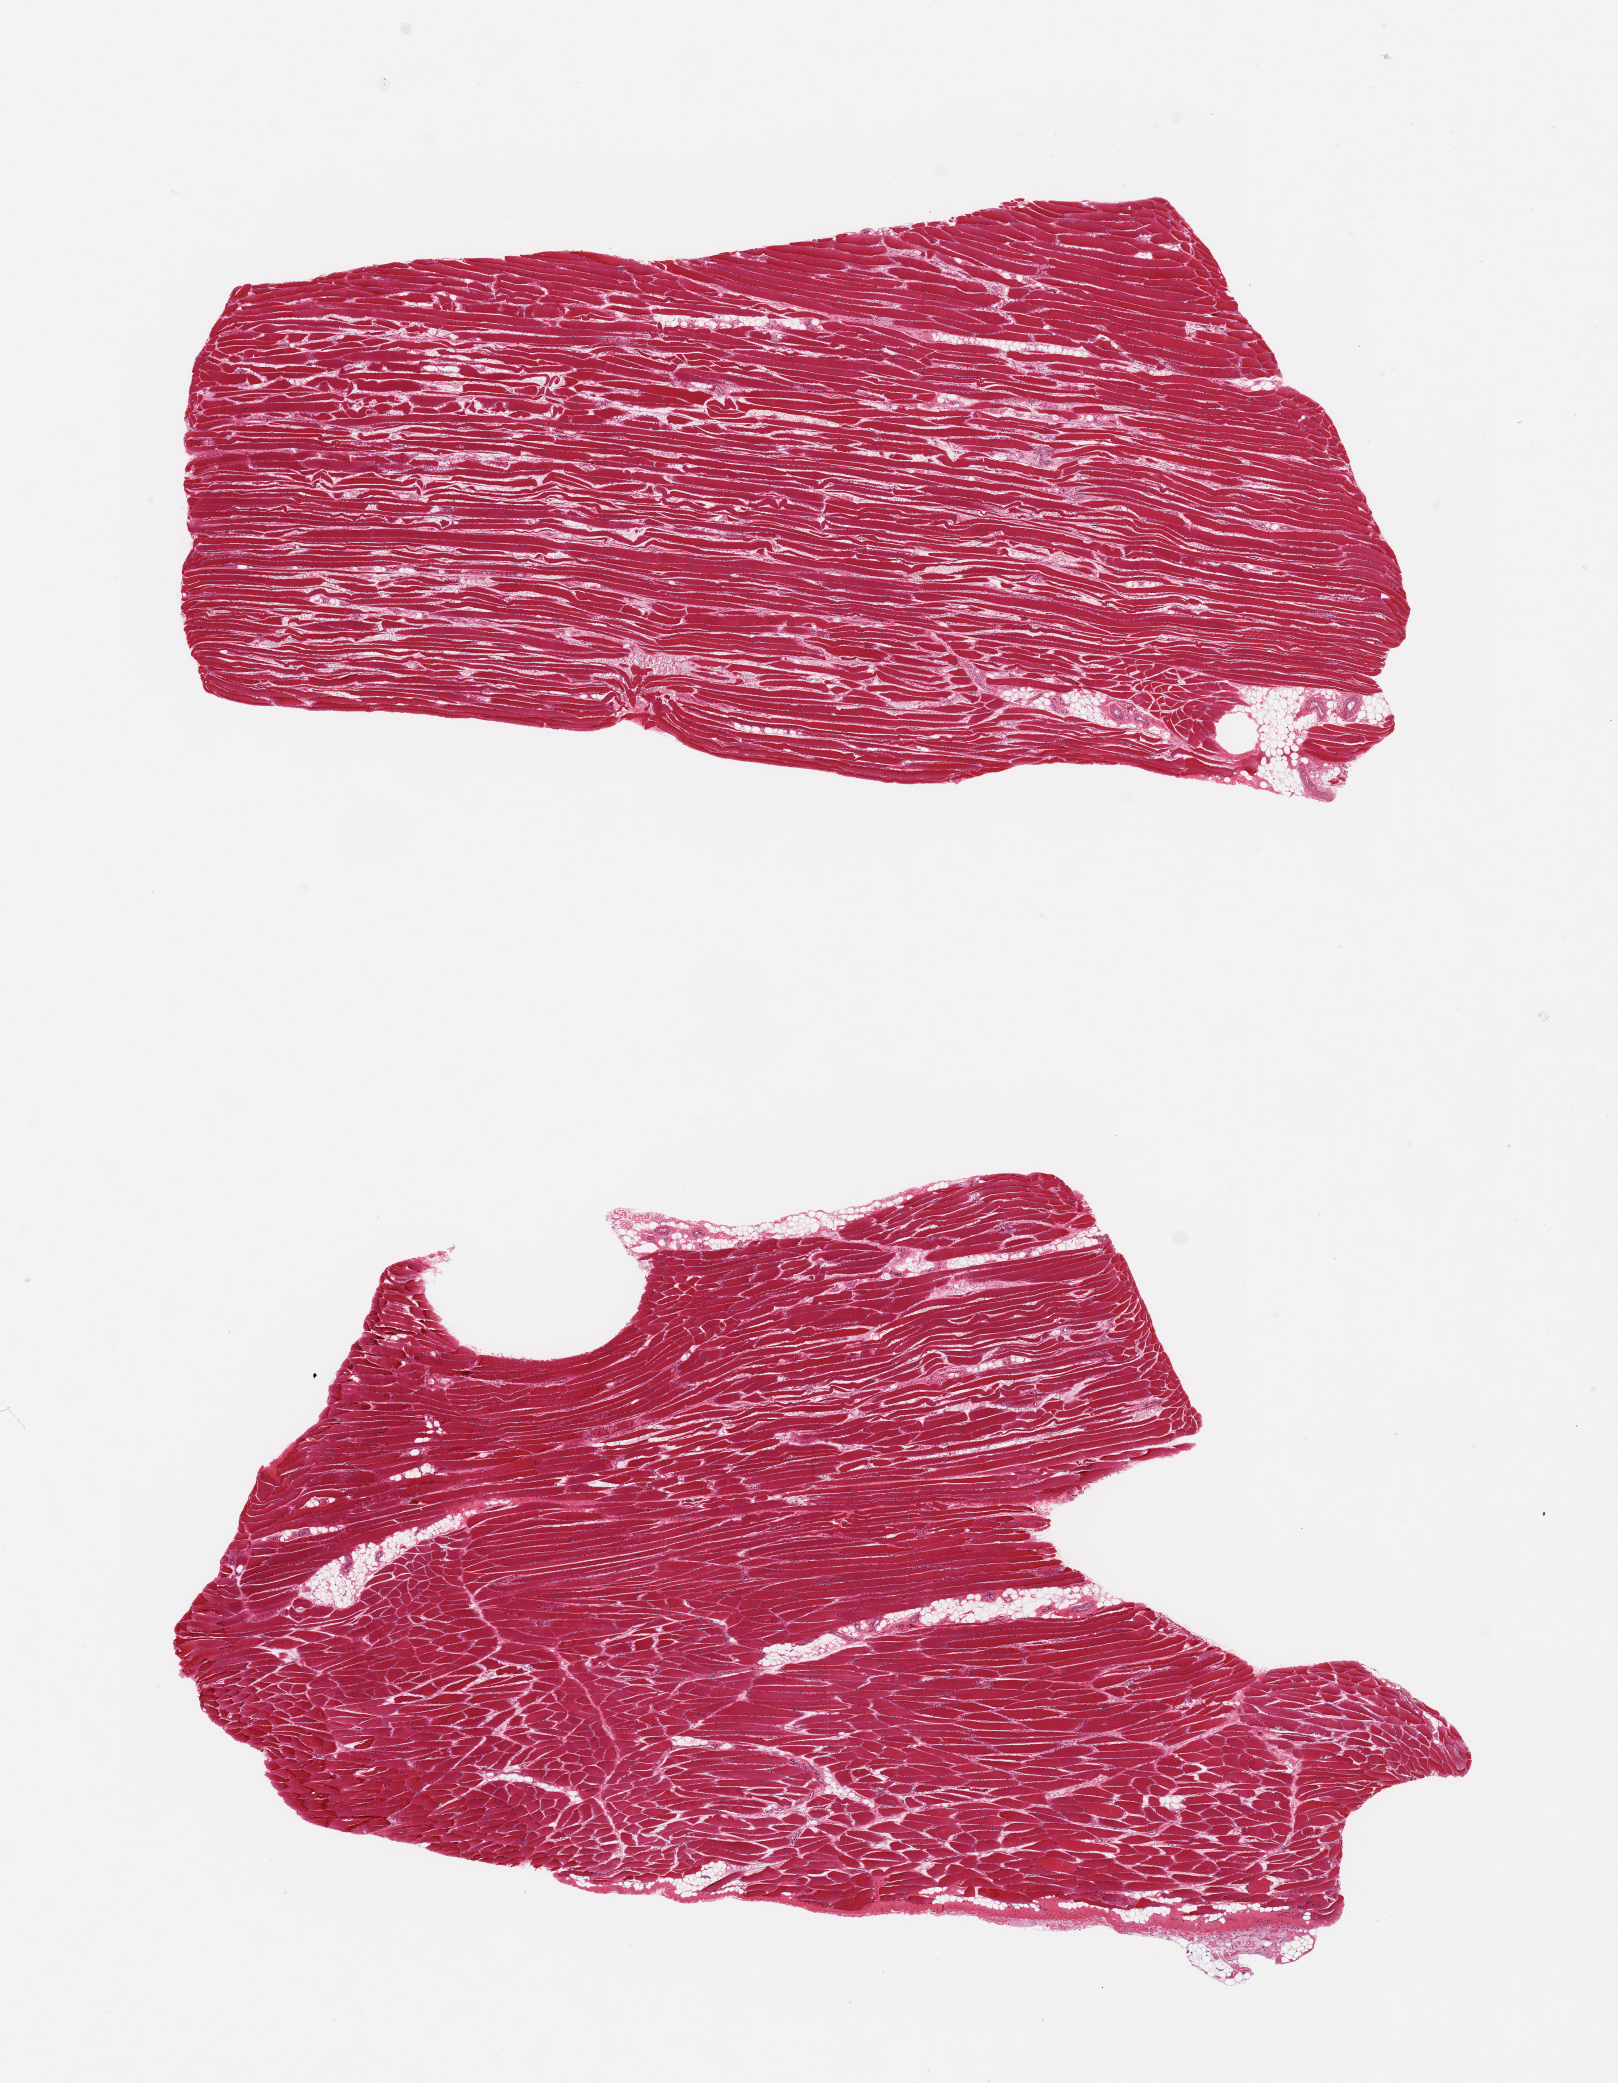
Whole-slide image, haematoxylin and eosin stain — a low-resolution overview of the entire scanned area, about 12.8 x 16.5 mm (acquisition: 20x scan). PAXgene-fixed, paraffin-embedded tissue. Sampled site (target tissue): skeletal muscle. Tissue donor sample. Male donor.
- review note (as recorded): 2 pieces; 10x5 & 10x6mm; free of adipose